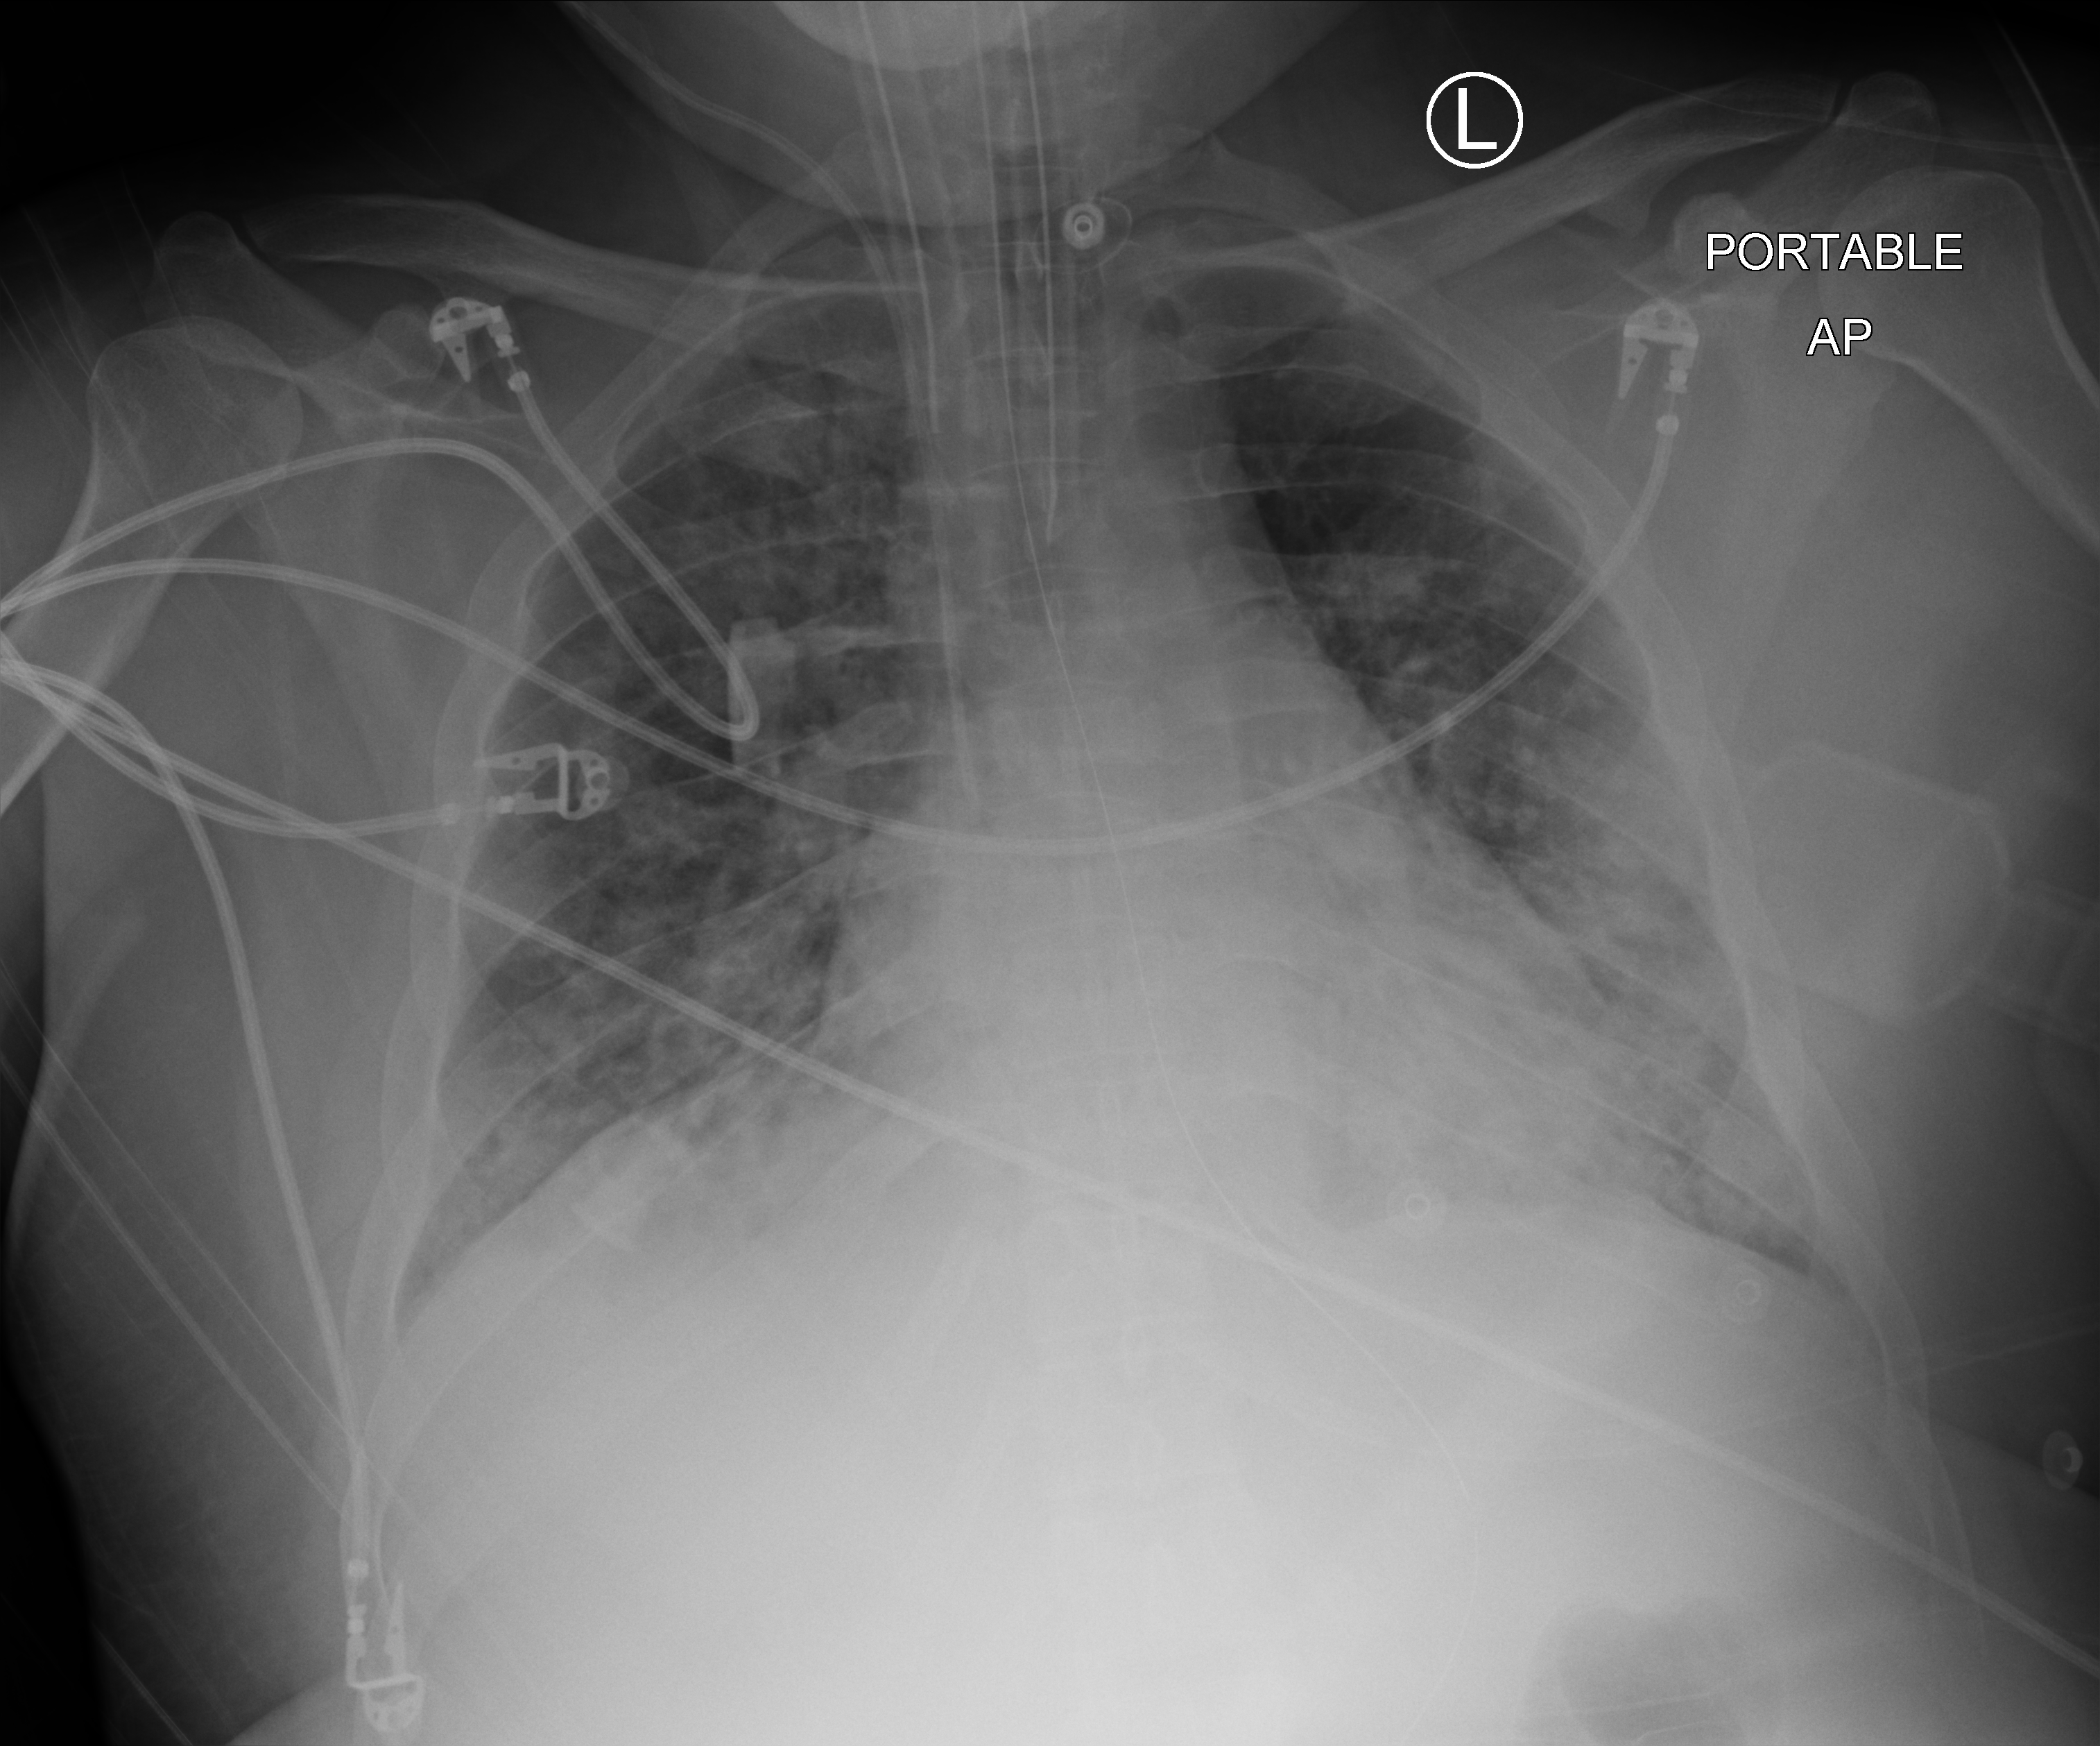
Portable chest radiograph; anteroposterior (AP) projection. Patient hospitalised with COVID-19, aged 18–59 years.
Hospital-stay facts (about this admission, not read from this image; timing relative to this image not recorded): length of hospital stay: 15 days; mechanically ventilated during this hospital stay: yes; admitted to intensive care during this hospital stay: yes.